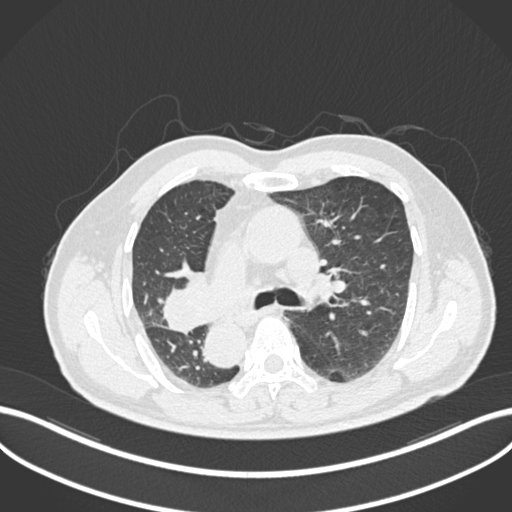
Chest CT, one axial slice; slice 148 of 206 in the series (ordered by position); reconstruction kernel B30f; 120 kVp; lung window (W 1500 / L -600 HU); 1 mm slice thickness; 512 × 512 image matrix, field of view 400 × 400 mm. Male patient, age 67 years. Case-level facts recorded for this patient, not image findings: clinical TNM (as recorded): T2a N0 M0.
Structures marked on this image (bounding box drawn by a radiologist):
- lung tumour (recorded histology: squamous cell carcinoma): bounding box <159,267,215,333> (left, top, right, bottom; pixels)